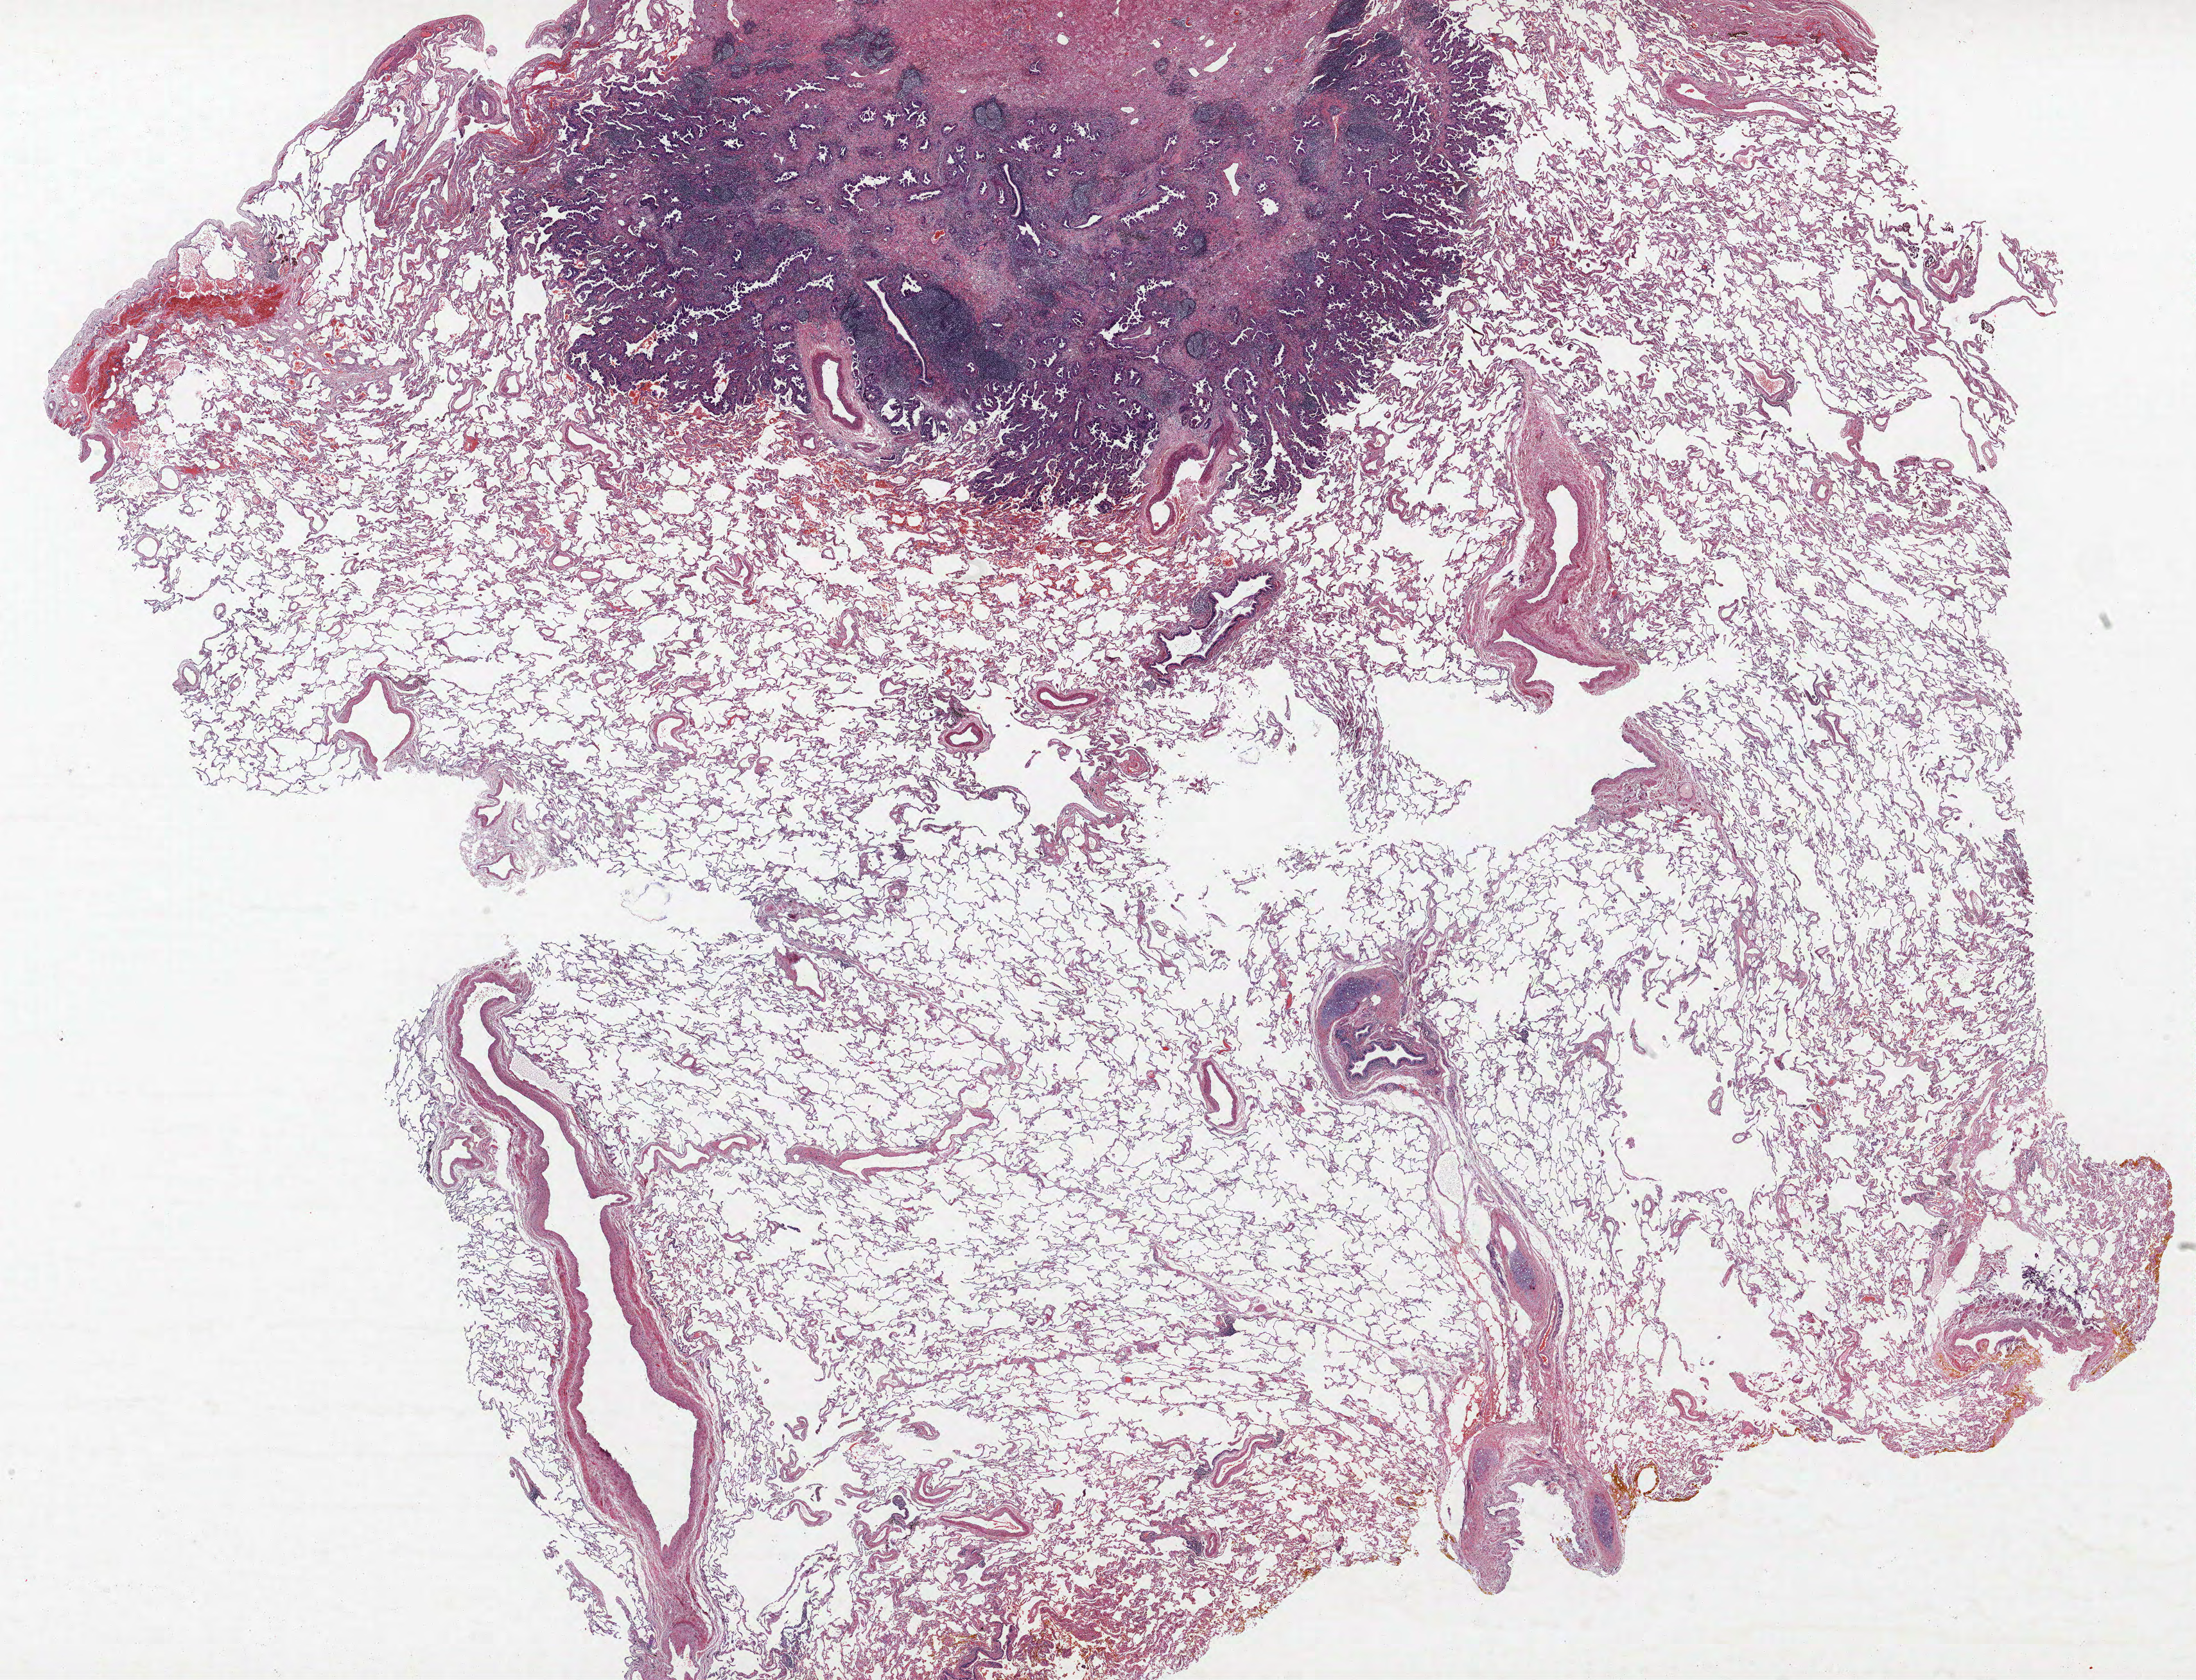
Whole-slide histology image, Hematoxylin and eosin (H&E) stained — shown as a low-resolution overview of the whole scanned area (about 27.4 x 20.9 mm, from a 40x scan), FFPE section, lung tissue. Male, age 56 at enrolment. Former smoker at enrolment. Grade: moderately differentiated (G2).
Tumour size (pathology): 9 mm. Stage (AJCC 6th edition): IA. Participant's lung-cancer diagnosis: Adenocarcinoma, NOS. Primary tumour location (clinical record): right upper lobe.